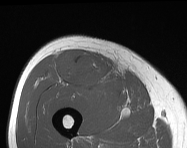
MRI of an extremity soft-tissue mass, one axial slice; MR volume resampled by the dataset authors to the PET/CT grid (not the native acquisition matrix); 187 × 148 image matrix. Male patient. Case-level facts recorded for this patient, not image findings: histological type: pleiomorphic leiomyosarcoma; grade: intermediate; site of the primary tumour: right thigh.
Structures marked on this image (expert contour drawn on MRI and transferred to this co-registered scan by the dataset authors):
- gross tumour volume including surrounding oedema: bounding box <57,50,112,89> (left, top, right, bottom; pixels)
- gross tumour volume (mass): <68,58,108,85>